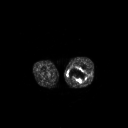
FDG PET of an extremity soft-tissue mass (from a PET/CT study), one axial slice; slice 223 of 267 in the series (ordered by position); 128 × 128 image matrix, field of view 700 × 700 mm. Patient: male, 44 years. From the clinical record (not read from this slice): histological type: undifferentiated pleomorphic liposarcoma; grade: high; site of the primary tumour: left thigh.
Structures marked on this image (expert contour drawn on MRI and transferred to this co-registered scan by the dataset authors):
- gross tumour volume including surrounding oedema: bounding box (x1, y1, x2, y2) in pixels: (68, 67, 87, 83)
- gross tumour volume (mass): (68, 67, 87, 83)